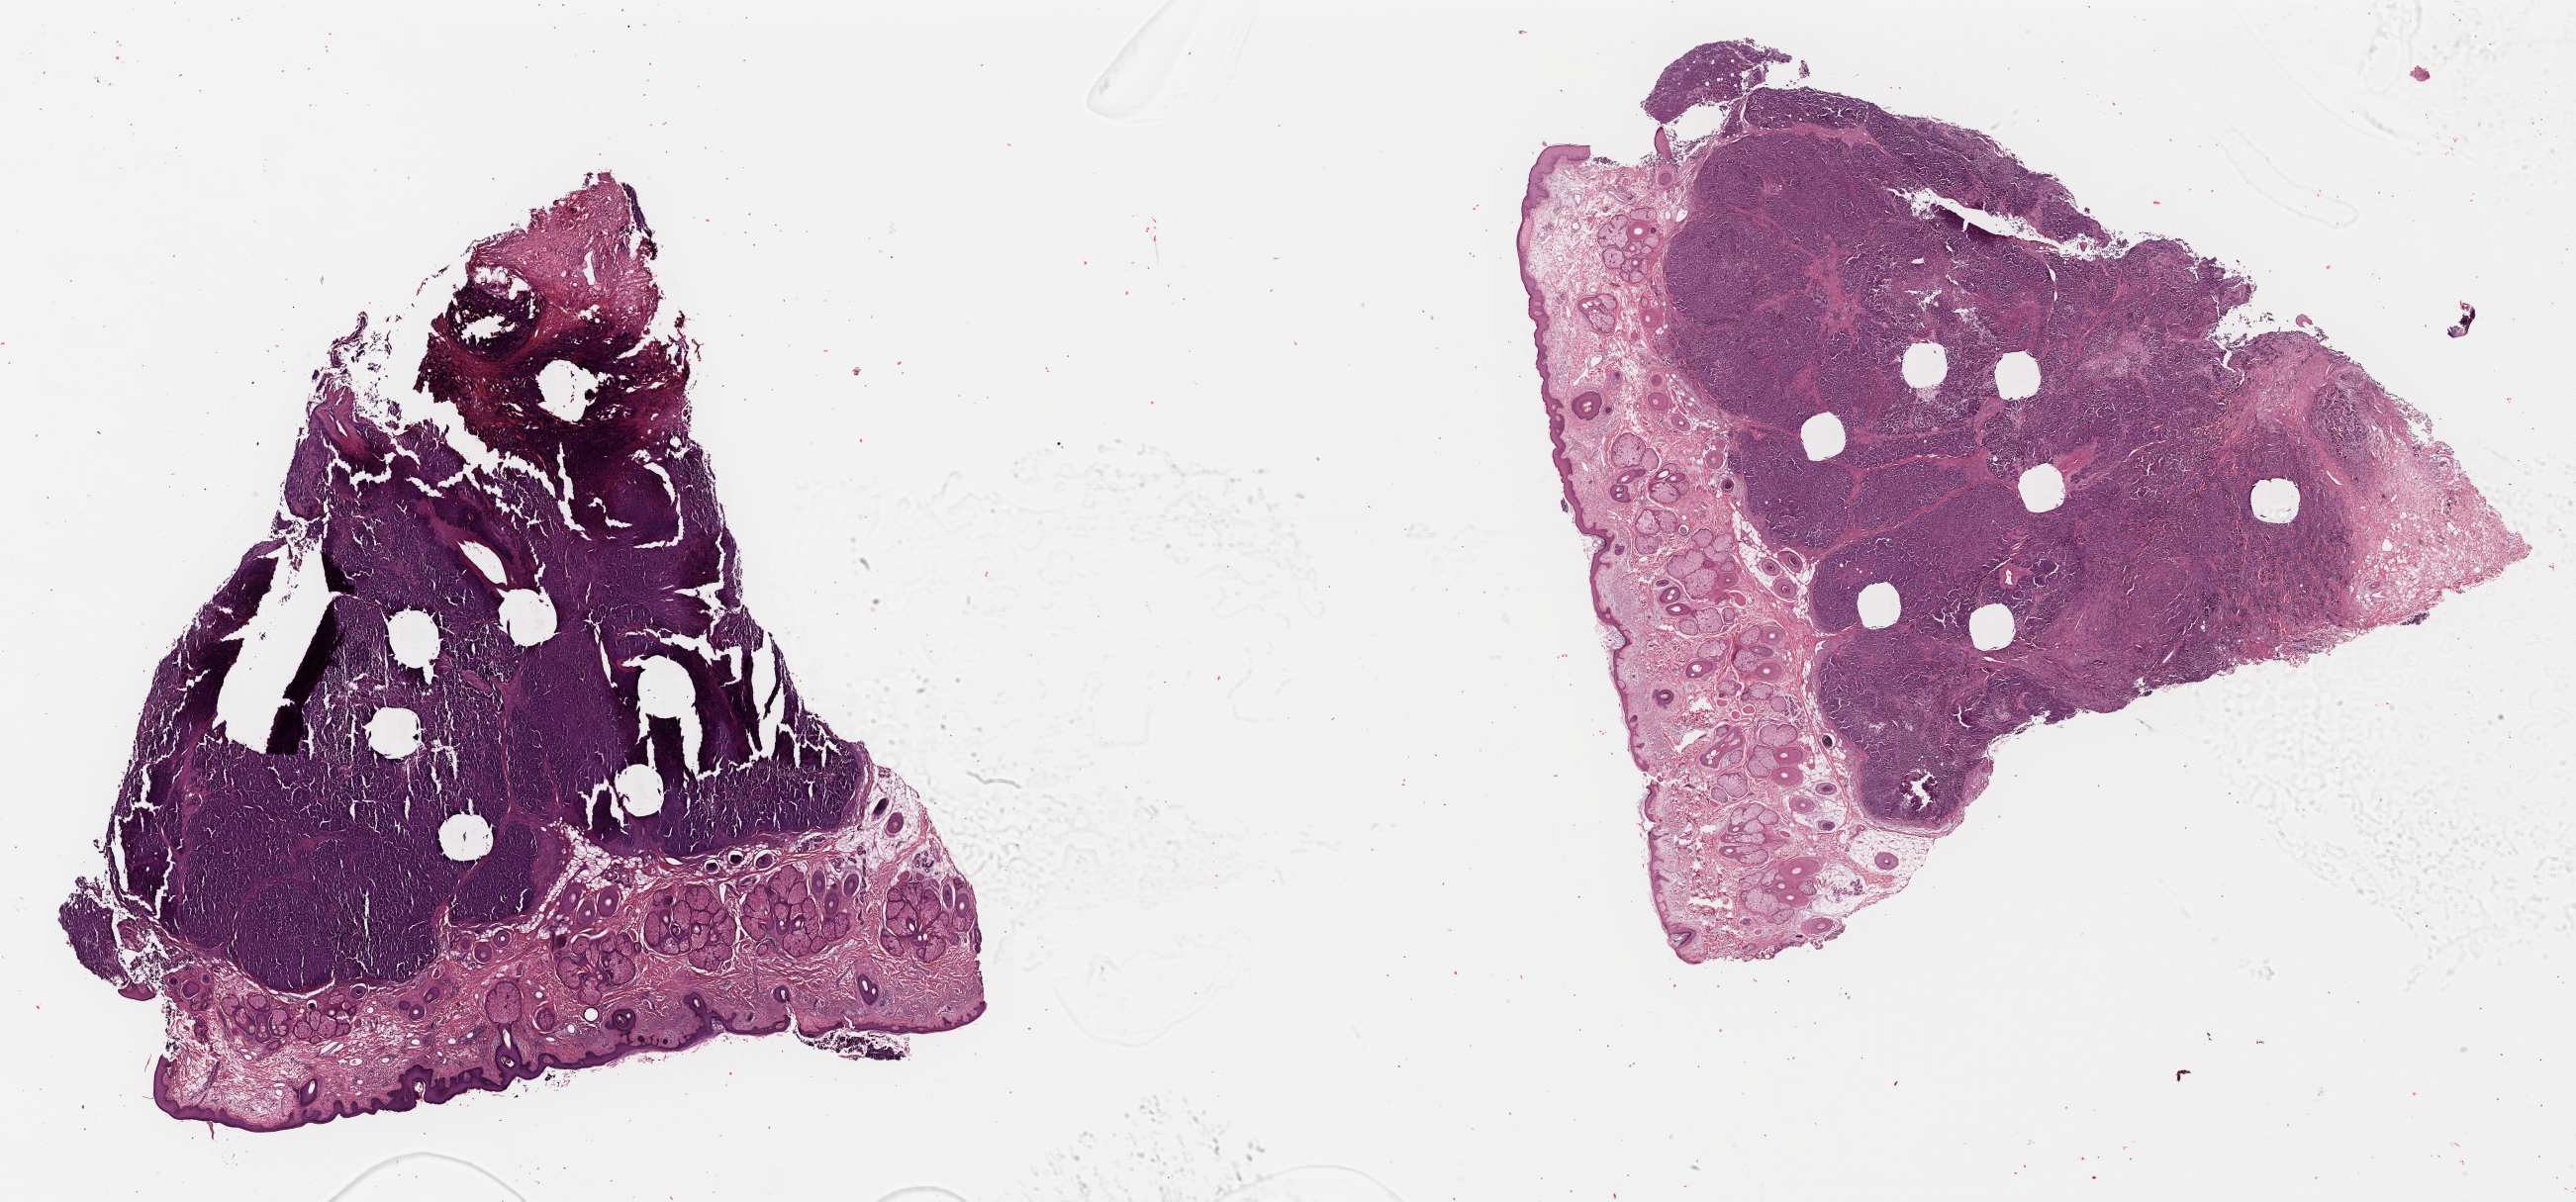
Whole-slide histology image, Hematoxylin and eosin (H&E) stained — low-resolution overview of the scanned area, about 40.9 x 19.1 mm (slide scanned at 40x), formalin-fixed paraffin-embedded (FFPE) diagnostic section, metastatic tumour sample, sampled site: skin. Male patient; age at initial diagnosis 51 years.
* this section: metastatic tumour tissue
* patient diagnosis: Malignant melanoma, NOS